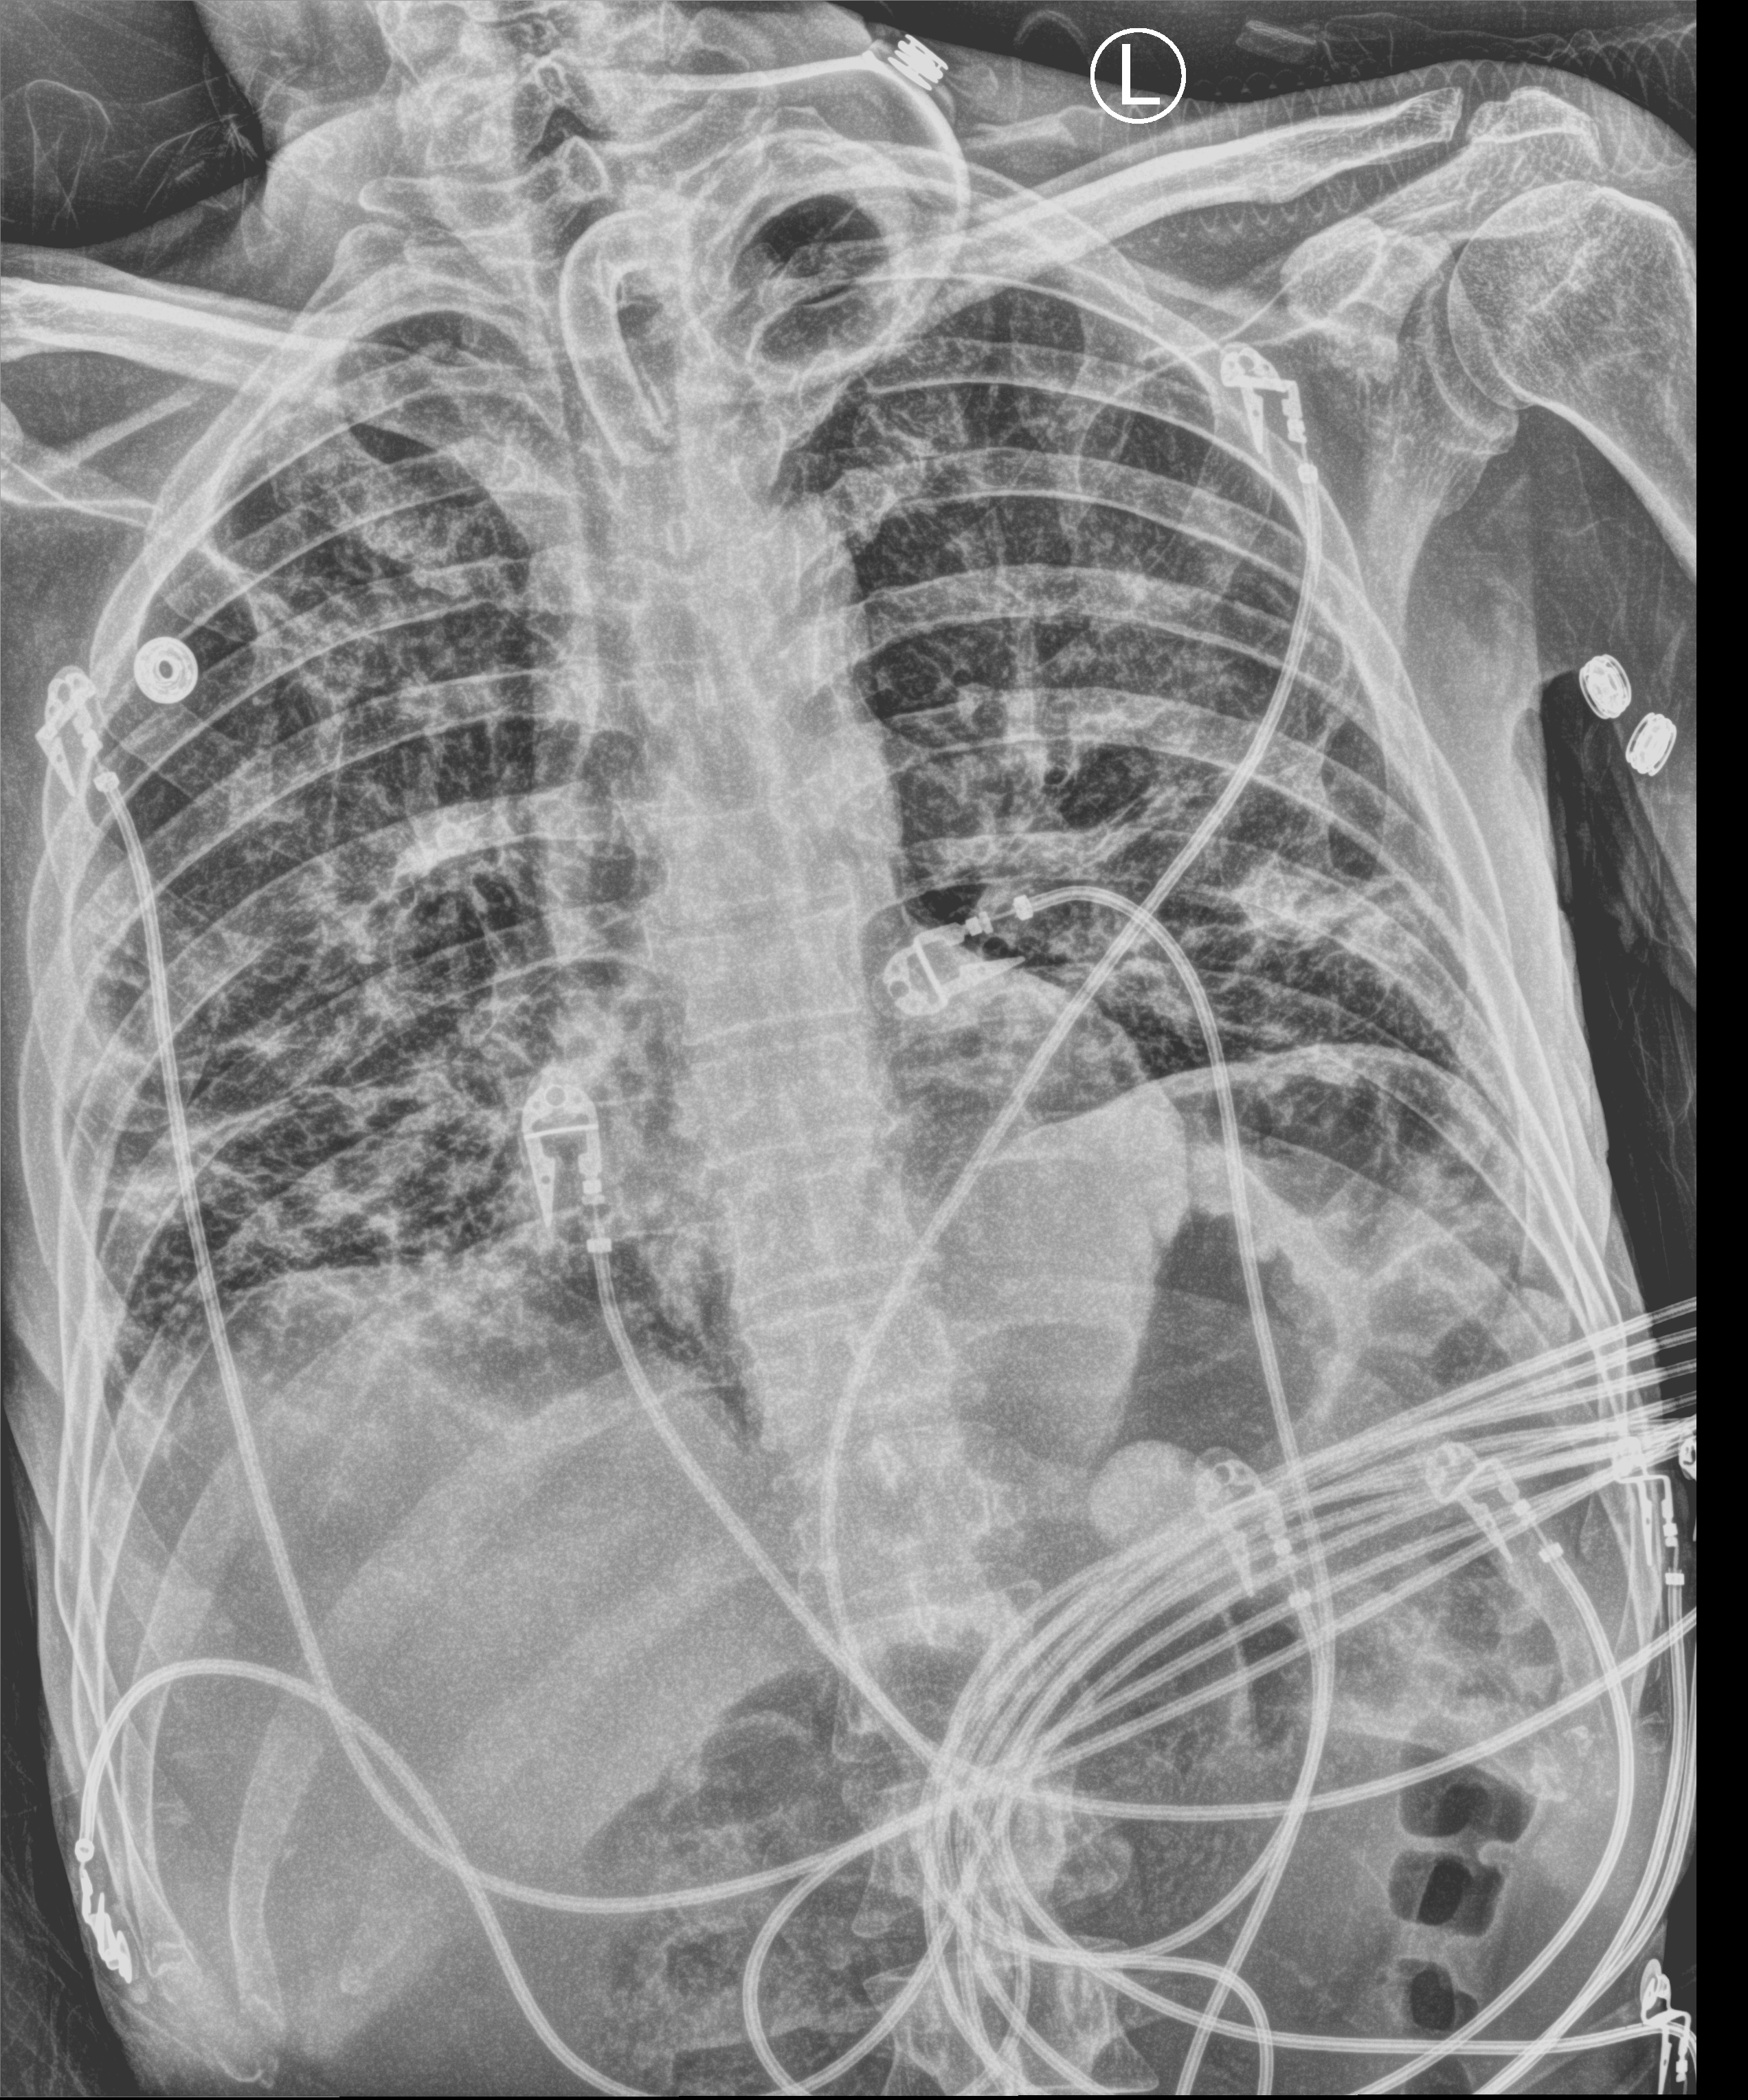
Bedside chest radiograph (computed radiography); anteroposterior (AP) projection. Male patient hospitalised with COVID-19, age 18–59 years.
Admission-level facts for this patient (not findings on this image; timing relative to this image not recorded): admitted to intensive care during this hospital stay: yes; mechanically ventilated during this hospital stay: yes.